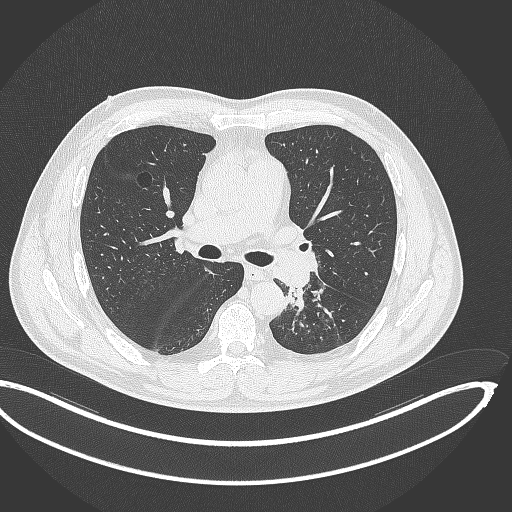
Chest CT, one axial slice; slice 212 of 362 in the series (ordered by position); reconstruction kernel B70f; lung window (W 1500 / L -600 HU); 512 × 512 image matrix, field of view 442 × 442 mm. Patient: male, 50 years. Case-level facts recorded for this patient, not image findings: clinical TNM (as recorded): T2a N3 M0.
Structures marked on this image (rectangle marked by the reading radiologist):
- lung tumour (recorded histology: squamous cell carcinoma): bounding box (x1, y1, x2, y2) in pixels: (282, 281, 308, 311)